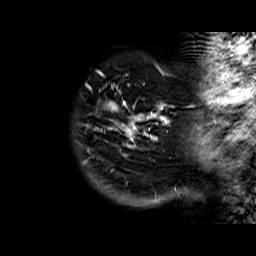
Breast MRI (dynamic contrast-enhanced), one sagittal slice; slice 4 of 60 in the series (ordered by position); dynamic contrast-enhanced series, time point 2 of 6 at this slice position (early post-contrast); 1.5 T; TE 6.3 ms, TR 32.4 ms; 256 × 256 image matrix. Female patient. Case-level facts recorded for this patient, not image findings: setting: breast cancer imaged before/during neoadjuvant chemotherapy; receptor status: HR-positive, HER2-negative.
Annotated regions visible in this slice (semi-automatic segmentation, software-assisted and operator-edited):
- analysis volume of interest (the breast-tissue region the enhancement analysis was run in; not a lesion): bounding box <78,72,174,183> (left, top, right, bottom; pixels)
- tumour enhancement mask (voxels above the 100 % enhancement threshold inside the analysis volume of interest): <86,72,169,156>